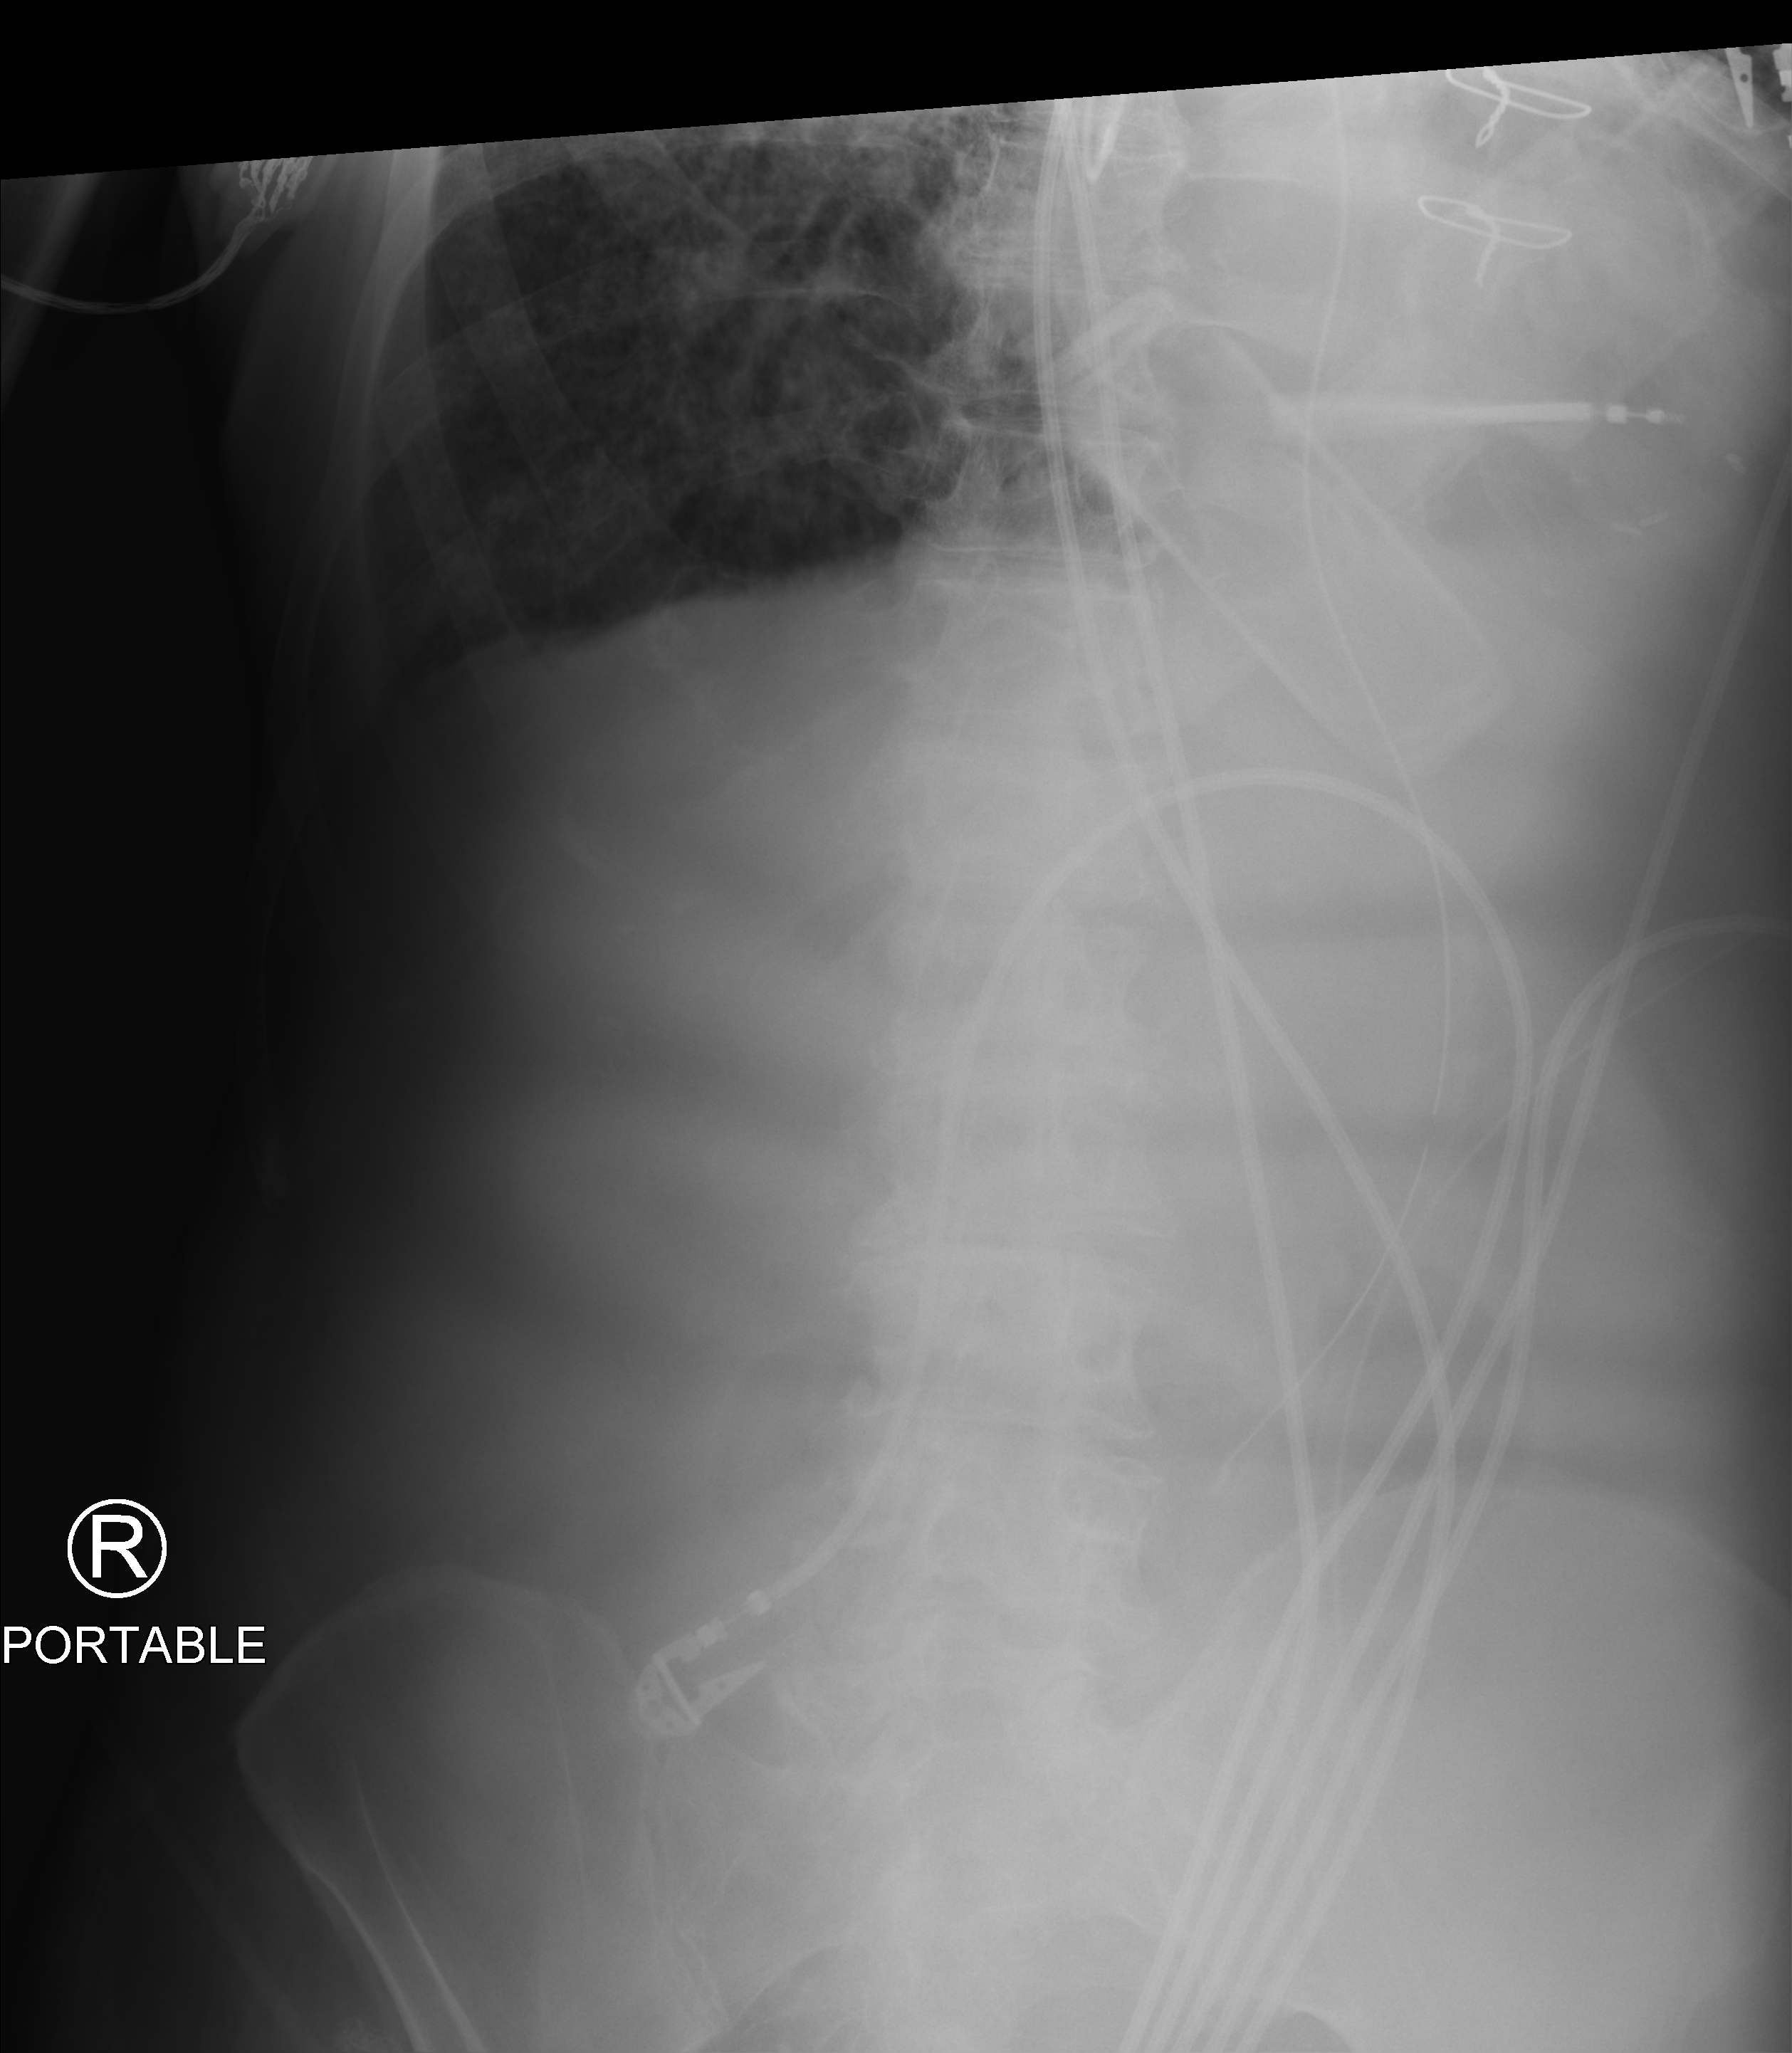
Abdomen X-ray (portable). Patient hospitalised with COVID-19; male, aged 75–90 years.
From the hospital-stay record, not from the radiograph (when in the stay this image was taken is not recorded): length of hospital stay: 11 days; mechanically ventilated during this hospital stay: yes; admitted to intensive care during this hospital stay: yes.